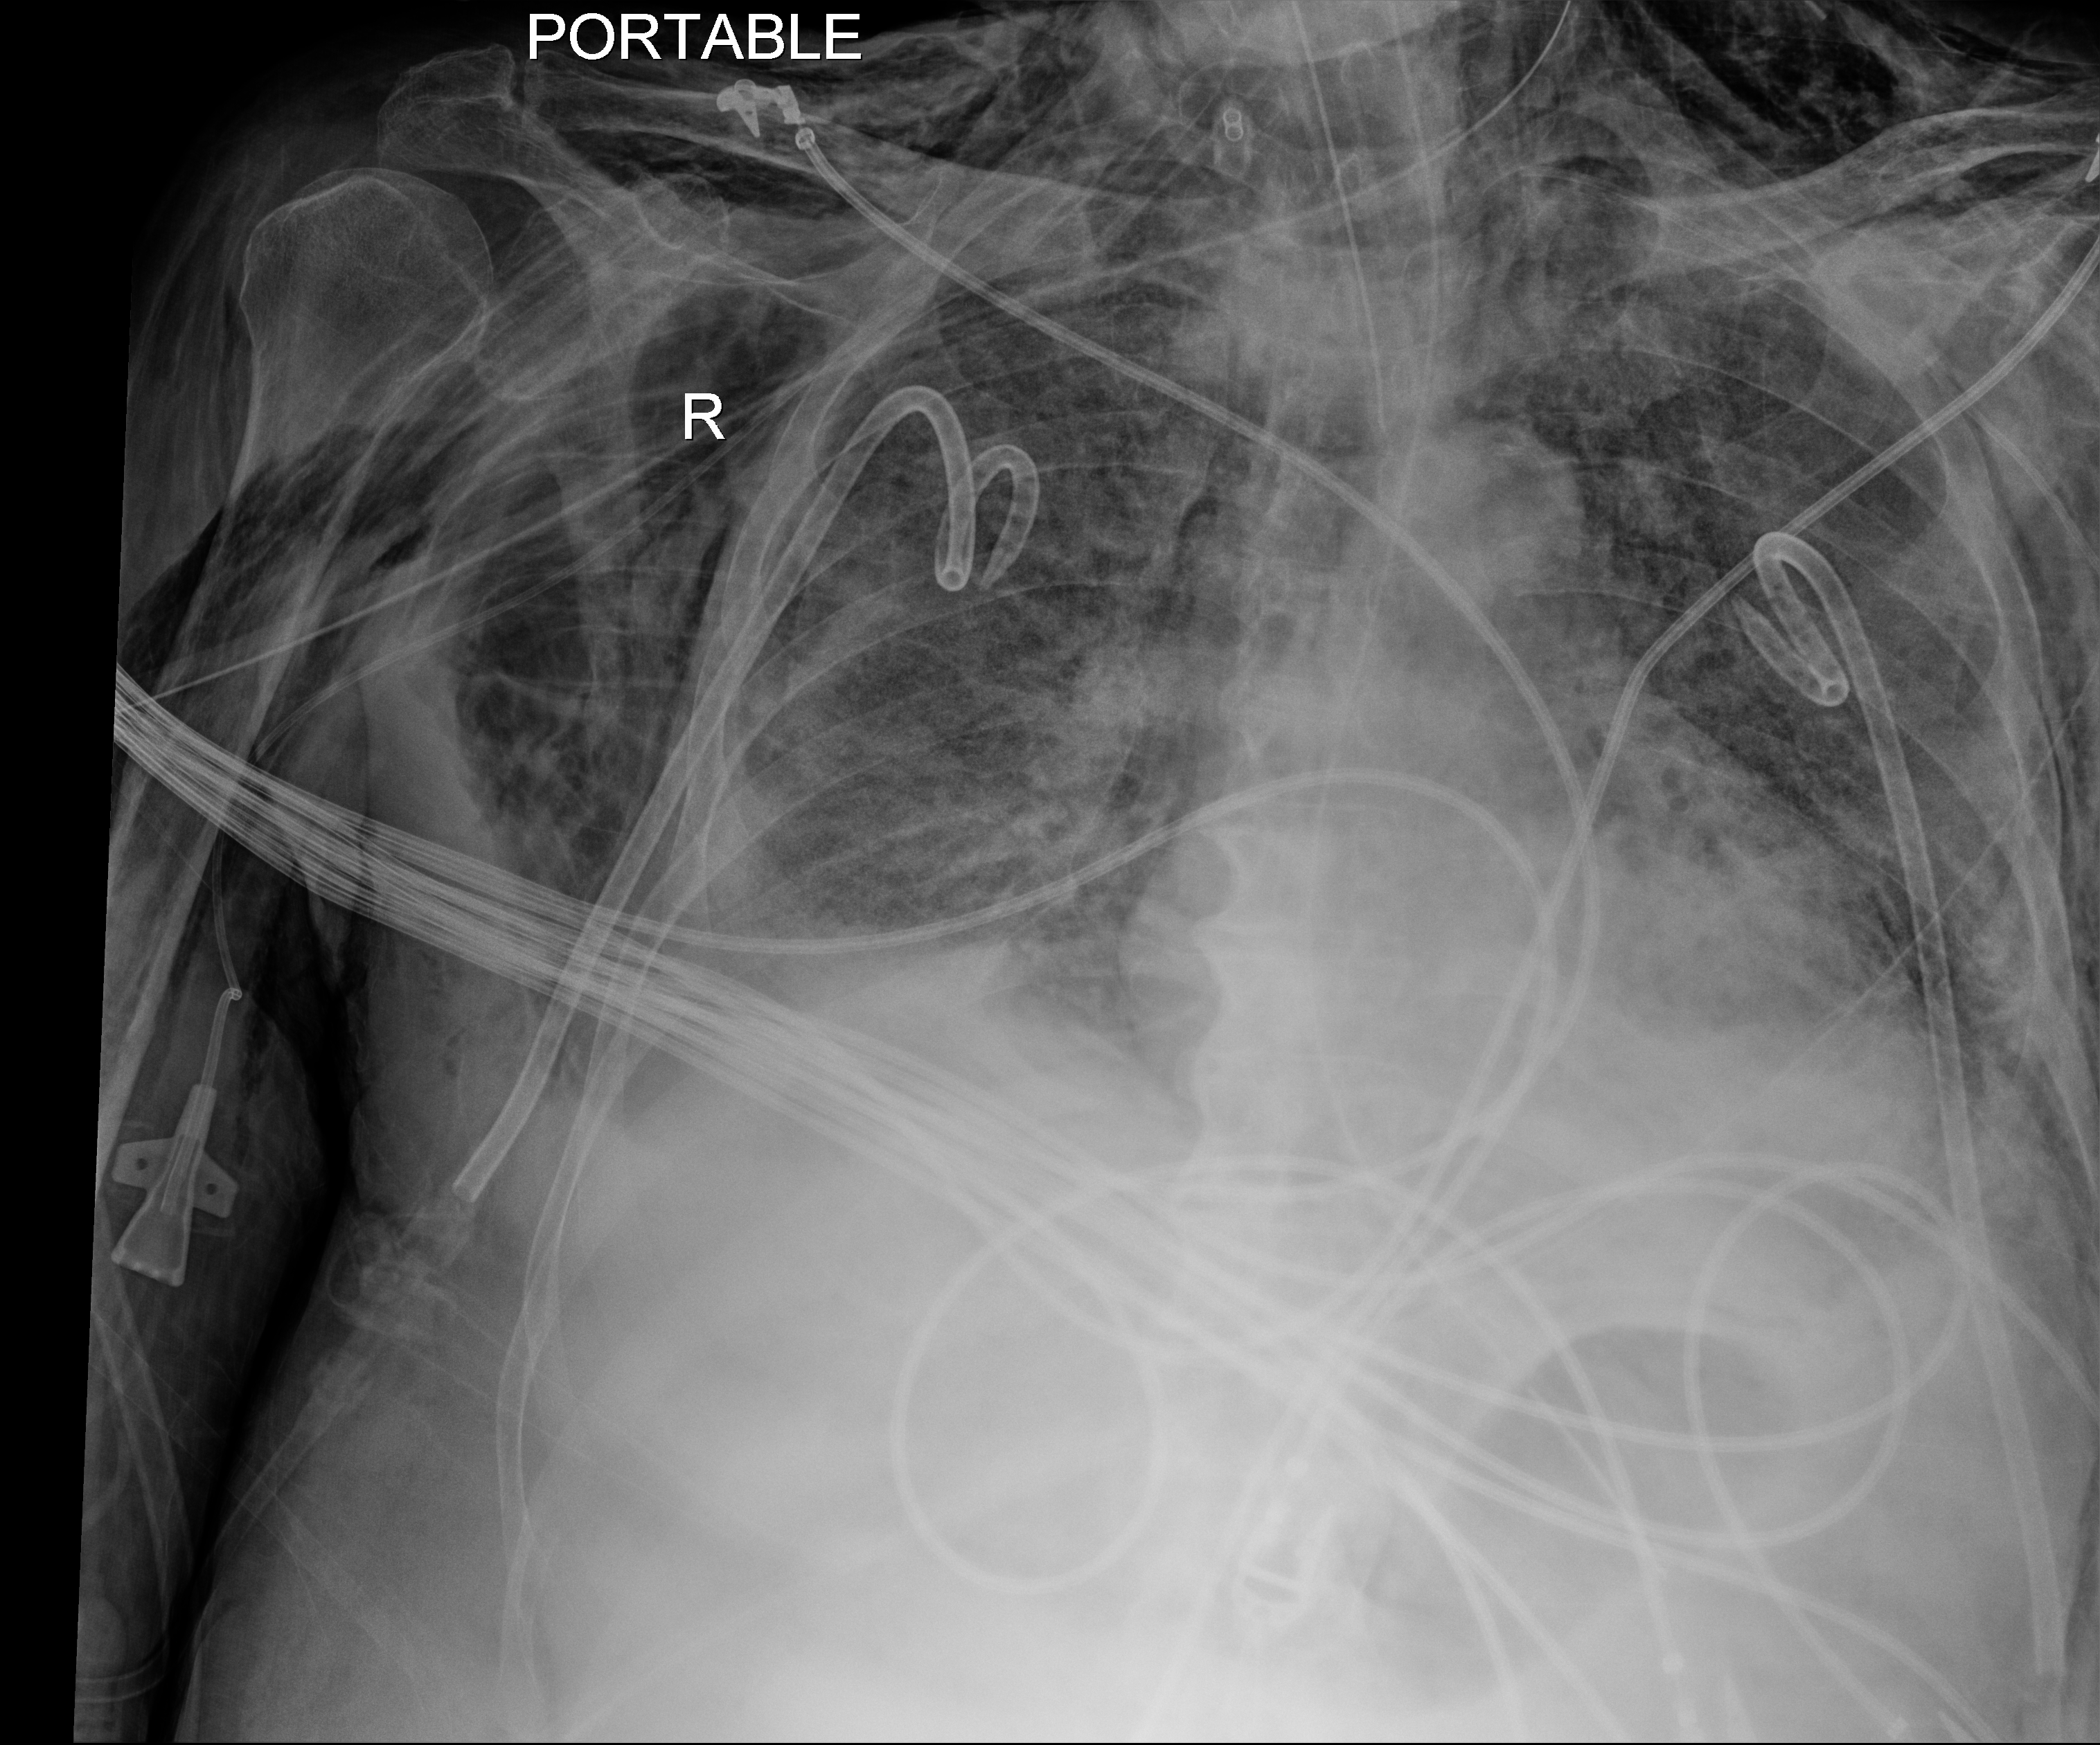
Portable chest radiograph; anteroposterior (AP) projection. Male patient hospitalised with COVID-19, age 75–90 years.
Admission-level facts for this patient (not findings on this image; timing relative to this image not recorded): mechanically ventilated during this hospital stay: yes; smoking status (admission record): never.